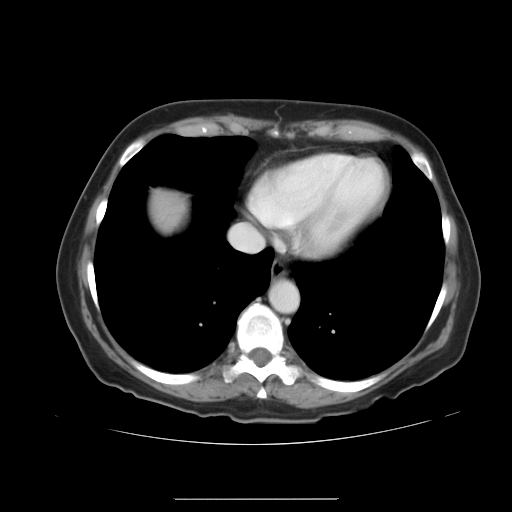
Contrast-enhanced abdominal CT, one axial slice; position 37 of 41 along the scan axis; 120 kVp; intravenous contrast given; soft-tissue window (W 400 / L 40 HU); 5 mm slice thickness; 512 × 512 image matrix, field of view 381 × 381 mm. Female patient, age 63 years. Case-level facts recorded for this patient, not image findings: diagnosis: colorectal cancer liver metastases, imaged before liver resection; multiple liver metastases: yes; largest metastasis: 1.5 cm; disease in both lobes: yes.
Outlined on this slice (outlined manually by an expert reader):
- liver: box from (x=151, y=190) to (x=190, y=230) px
- planned liver remnant (the part of the liver to remain after resection): (x=151, y=190)–(x=190, y=230)